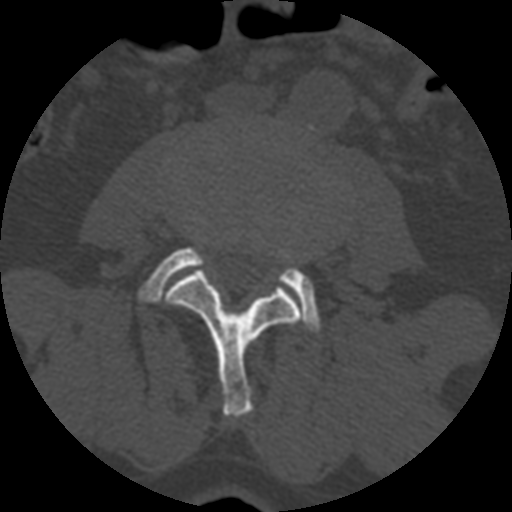
CT including the spine, one axial slice; position 296 of 399 along the scan axis; bone window (W 1800 / L 400 HU); 1.25 mm slice thickness; 512 × 512 image matrix. Patient age 71 years. From the clinical record (not read from this slice): primary cancer: prostate.
Outlined on this slice (semi-automatically segmented with operator editing):
- L3 vertebra: bounding box [x1, y1, x2, y2] px = [166, 268, 303, 418]
- L4 vertebra: [138, 247, 321, 335]